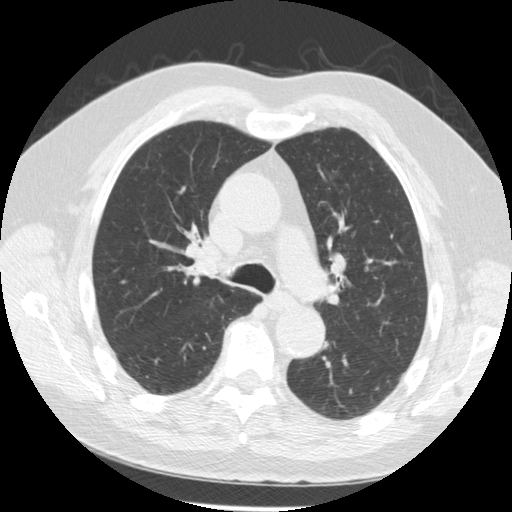
Low-dose screening chest CT, one axial slice; reconstruction kernel STANDARD; lung window (W 1500 / L -600 HU); 512 × 512 image matrix, field of view 355 × 355 mm.
Annotated regions visible in this slice (manually delineated by an expert):
- lesion 2 (tumor, hilum of right lung): box from (x=184, y=246) to (x=219, y=275) px